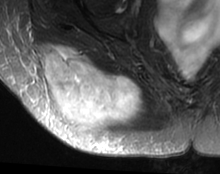
MRI of an extremity soft-tissue mass, one axial slice. Slice 20 of 63 in the series (ordered by position). T2-weighted fat-saturated. MR volume resampled by the dataset authors to the PET/CT grid (not the native acquisition matrix). 3.27 mm slice thickness. 220 × 174 image matrix, field of view 215 × 170 mm. Female patient. From the clinical record (not read from this slice): histological type: spindle cell suggestive of myxofibrosarcoma; grade: intermediate; site of the primary tumour: right buttock.
Outlined on this slice (expert contour drawn on MRI and transferred to this co-registered scan by the dataset authors):
- gross tumour volume (mass): bounding box (x1, y1, x2, y2) in pixels: (40, 45, 146, 140)